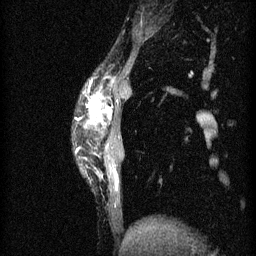
Breast MRI (dynamic contrast-enhanced), one sagittal slice; slice 10 of 60 in the series (ordered by position); 3 images stored at this slice position (order not interpretable as contrast timing); 1.5 T; TE 4.2 ms, TR 11 ms; 256 × 256 image matrix, field of view 180 × 180 mm. Female patient, age 40 years.
Annotated regions visible in this slice (semi-automatic segmentation, software-assisted and operator-edited):
- analysis volume of interest (the breast-tissue region the enhancement analysis was run in; not a lesion): bounding box (x1, y1, x2, y2) in pixels: (77, 82, 132, 191)
- tumour enhancement mask (voxels above the 70 % enhancement threshold inside the analysis volume of interest): (77, 94, 118, 189)